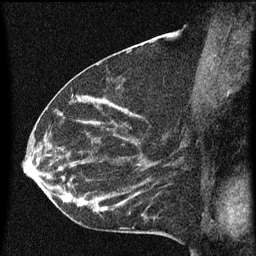
Breast MRI (dynamic contrast-enhanced), one sagittal slice. Position 31 of 60 along the scan axis. Dynamic contrast-enhanced series, image 2 of 3 at this slice position (ordered by acquisition). 1.5 T. TE 4.2 ms, TR 8 ms. 2 mm slice thickness. 256 × 256 image matrix, field of view 180 × 180 mm. Female patient, age 55 years.
Structures marked on this image (semi-automatic segmentation, software-assisted and operator-edited):
- analysis volume of interest (the breast-tissue region the enhancement analysis was run in; not a lesion): box from (x=51, y=156) to (x=145, y=217) px
- tumour enhancement mask (voxels above the 70 % enhancement threshold inside the analysis volume of interest): (x=52, y=160)–(x=140, y=213)